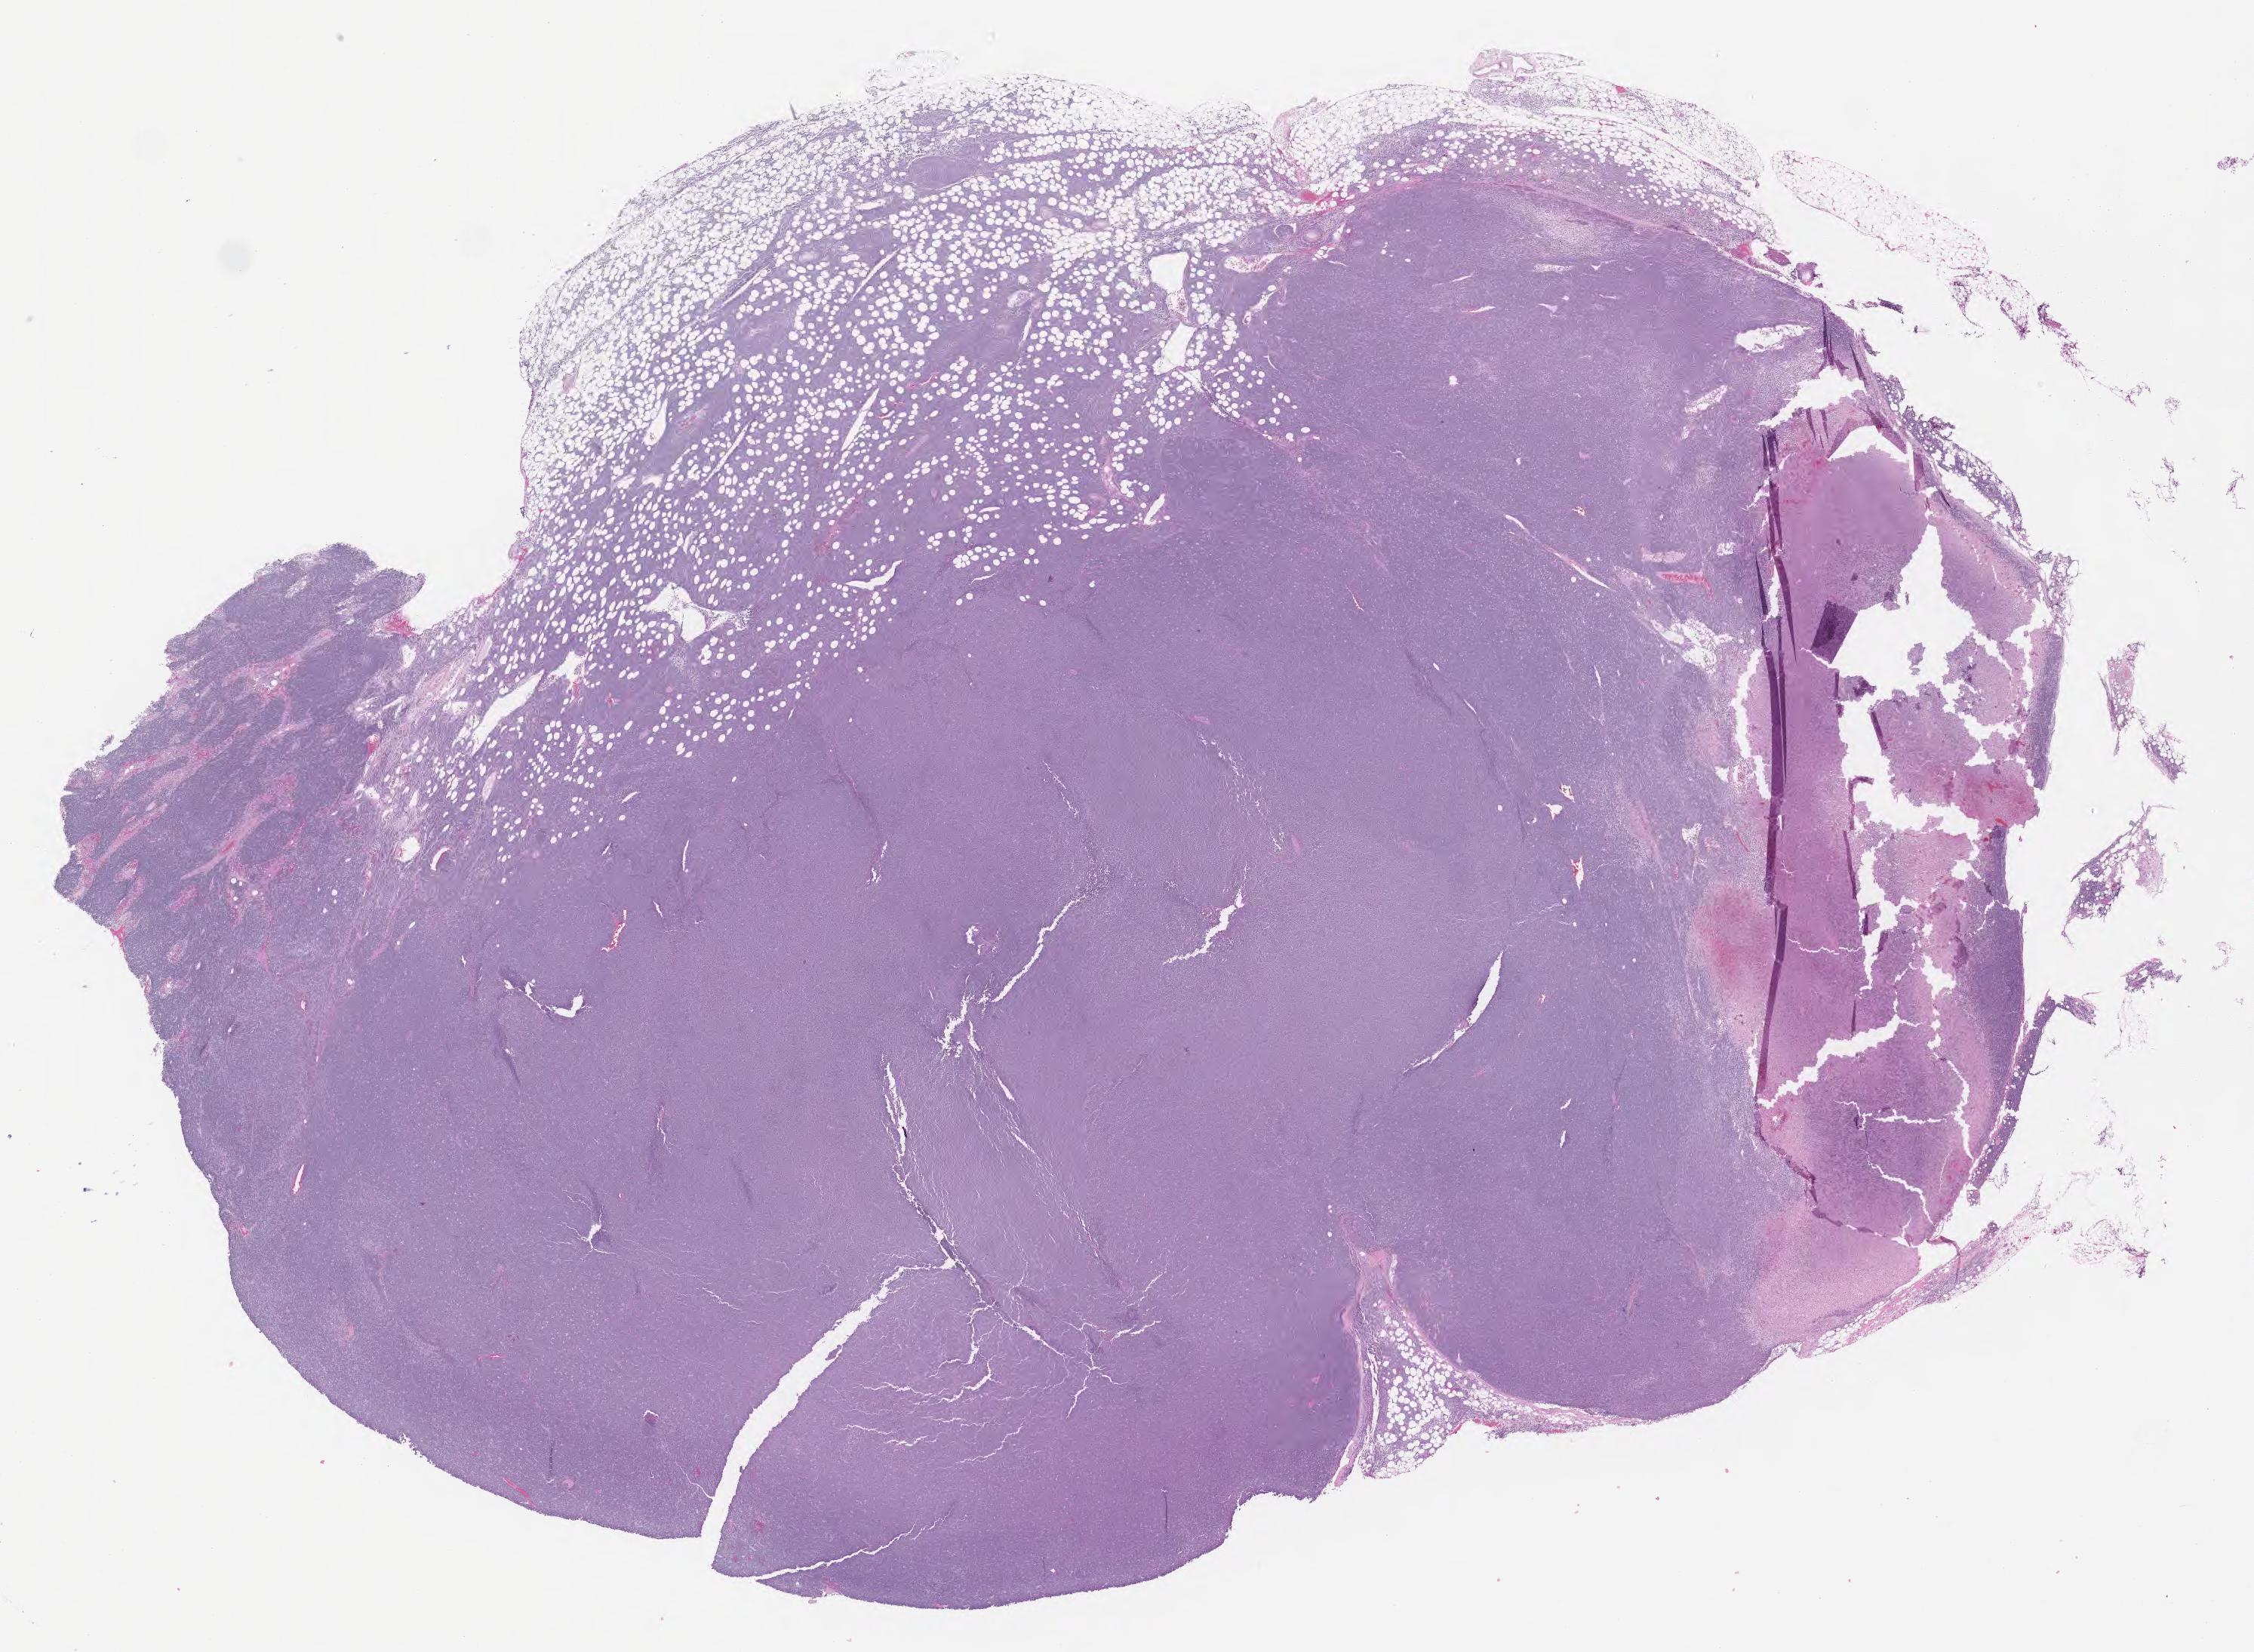
H&E whole-slide image — low-resolution overview of the scanned area, about 24.2 x 17.7 mm, specimen: tumor tissue. Male patient, 57 years old.
Diagnosis: Burkitt lymphoma, NOS.